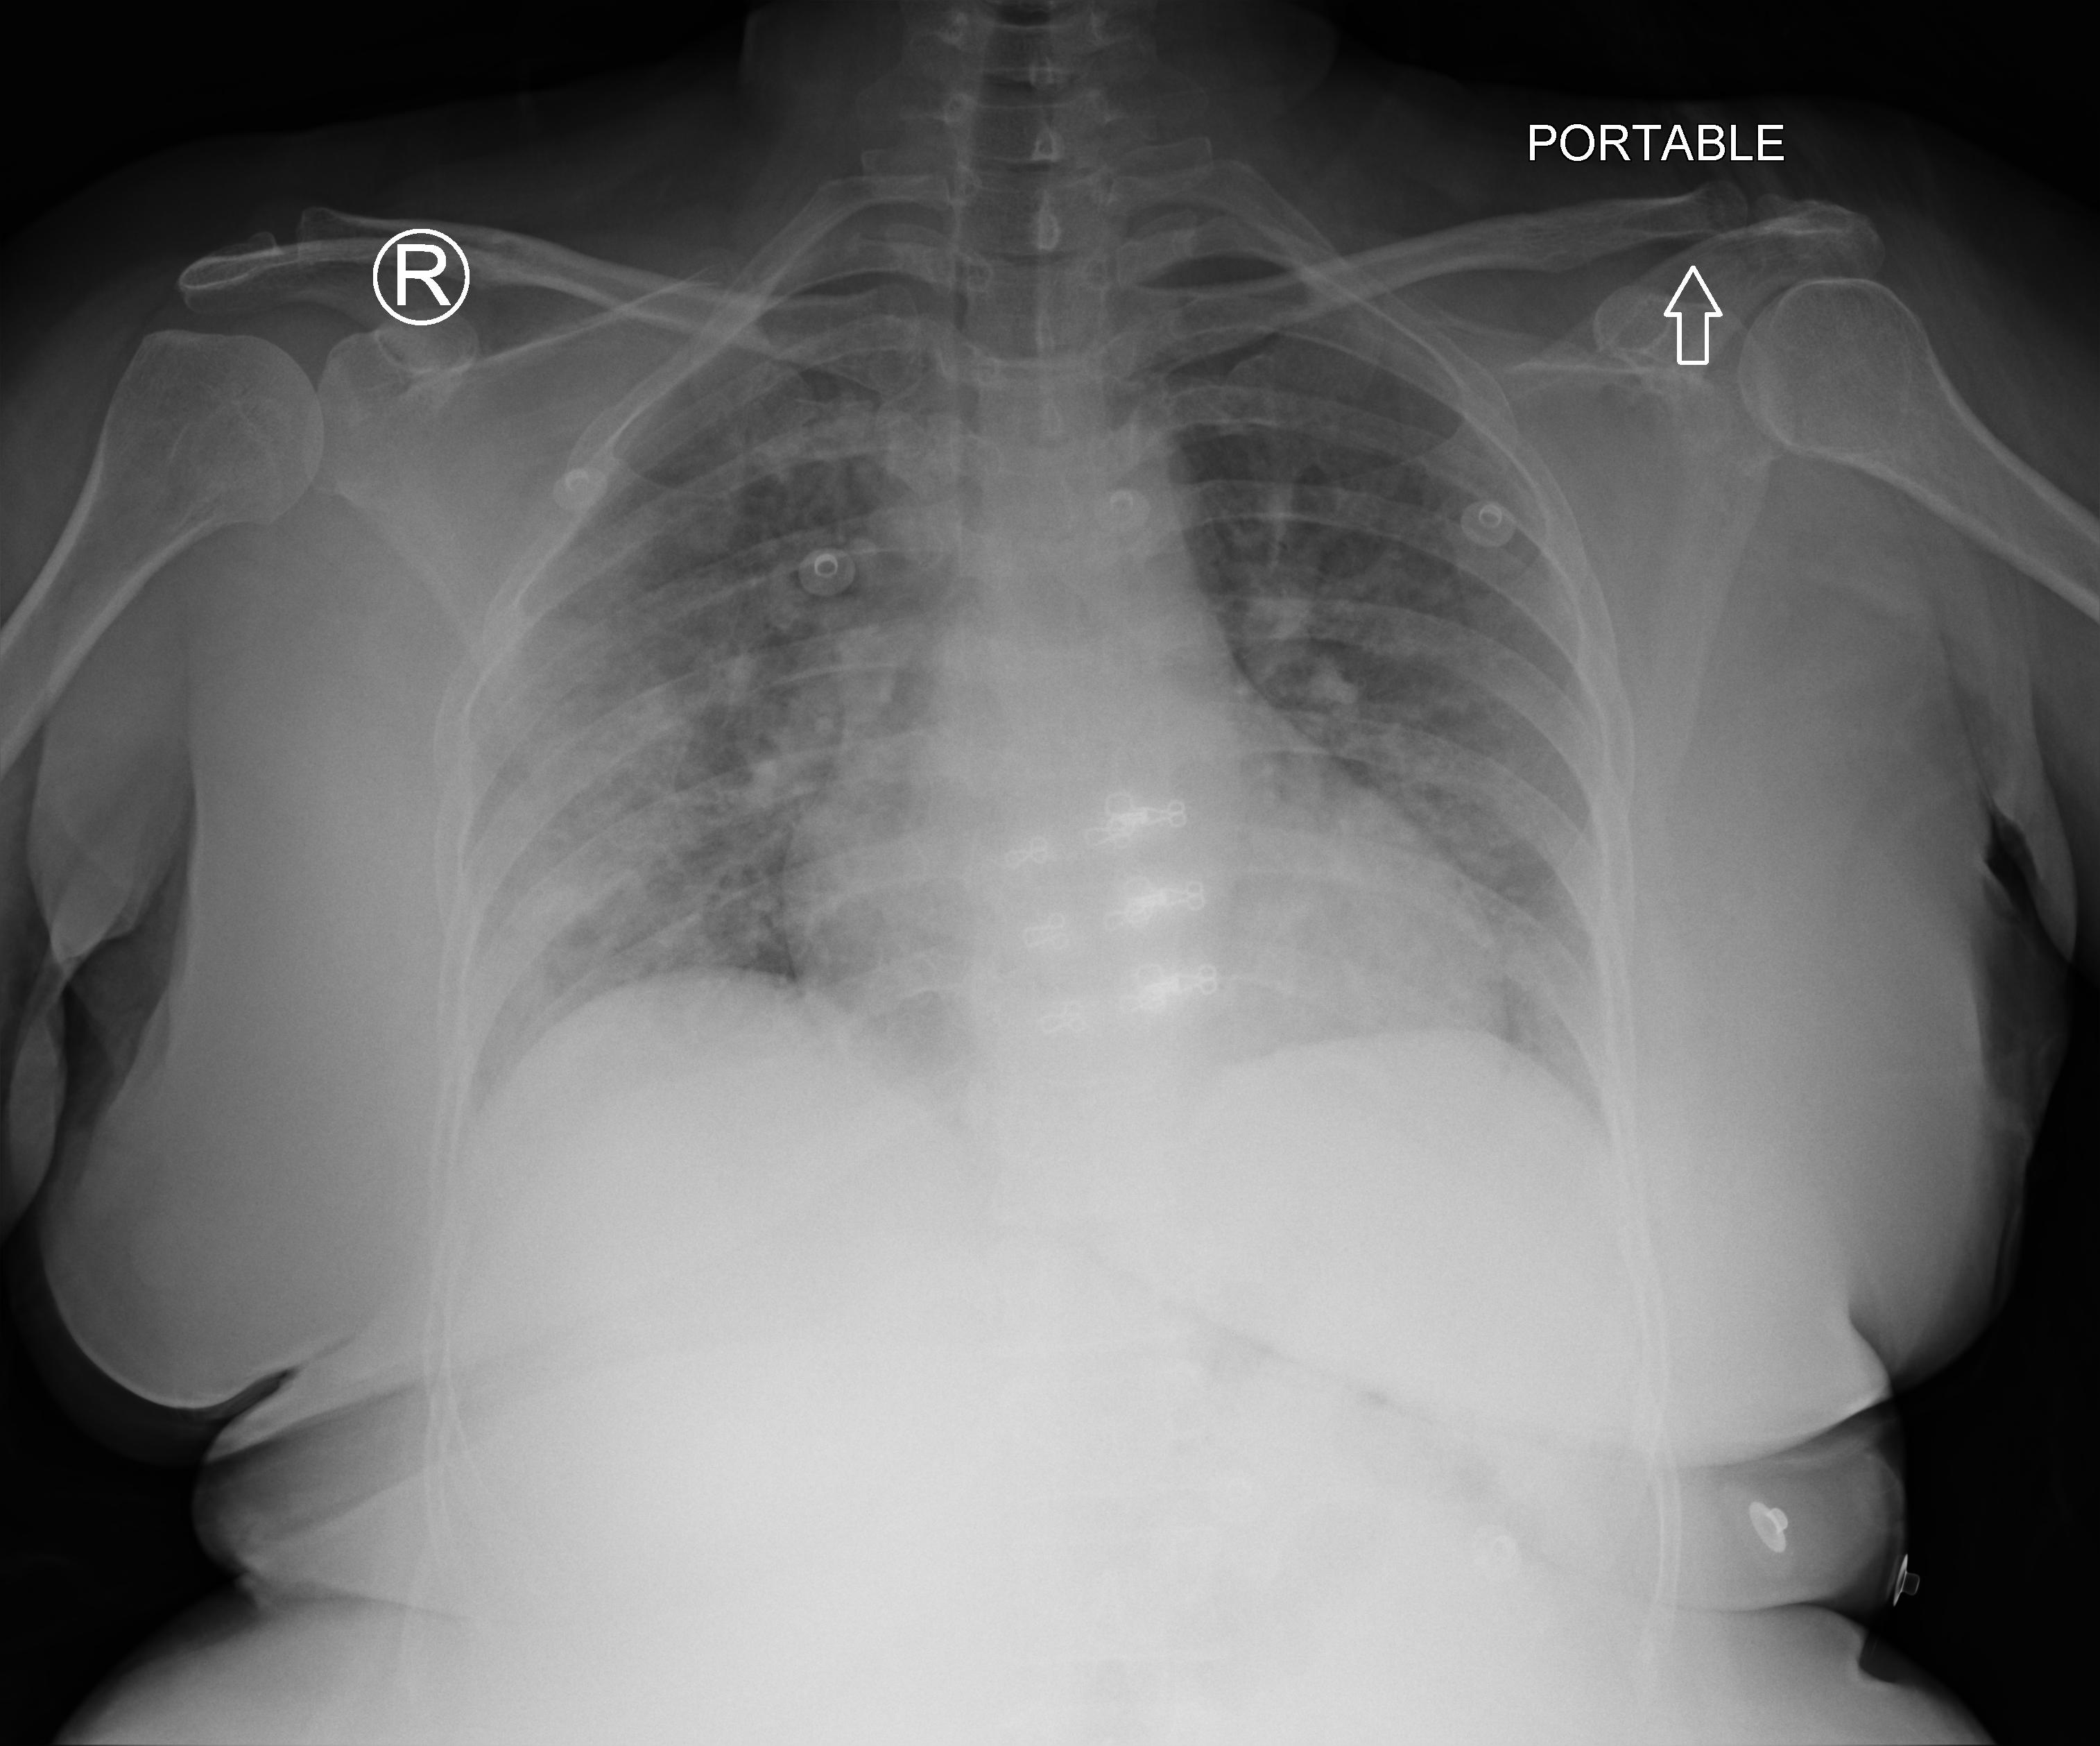
Portable chest radiograph, anteroposterior (AP) projection. Patient hospitalised with COVID-19; female, aged 18–59 years.
Hospital-stay facts (about this admission, not read from this image; timing relative to this image not recorded): smoking status (admission record): never; admitted to intensive care during this hospital stay: no.